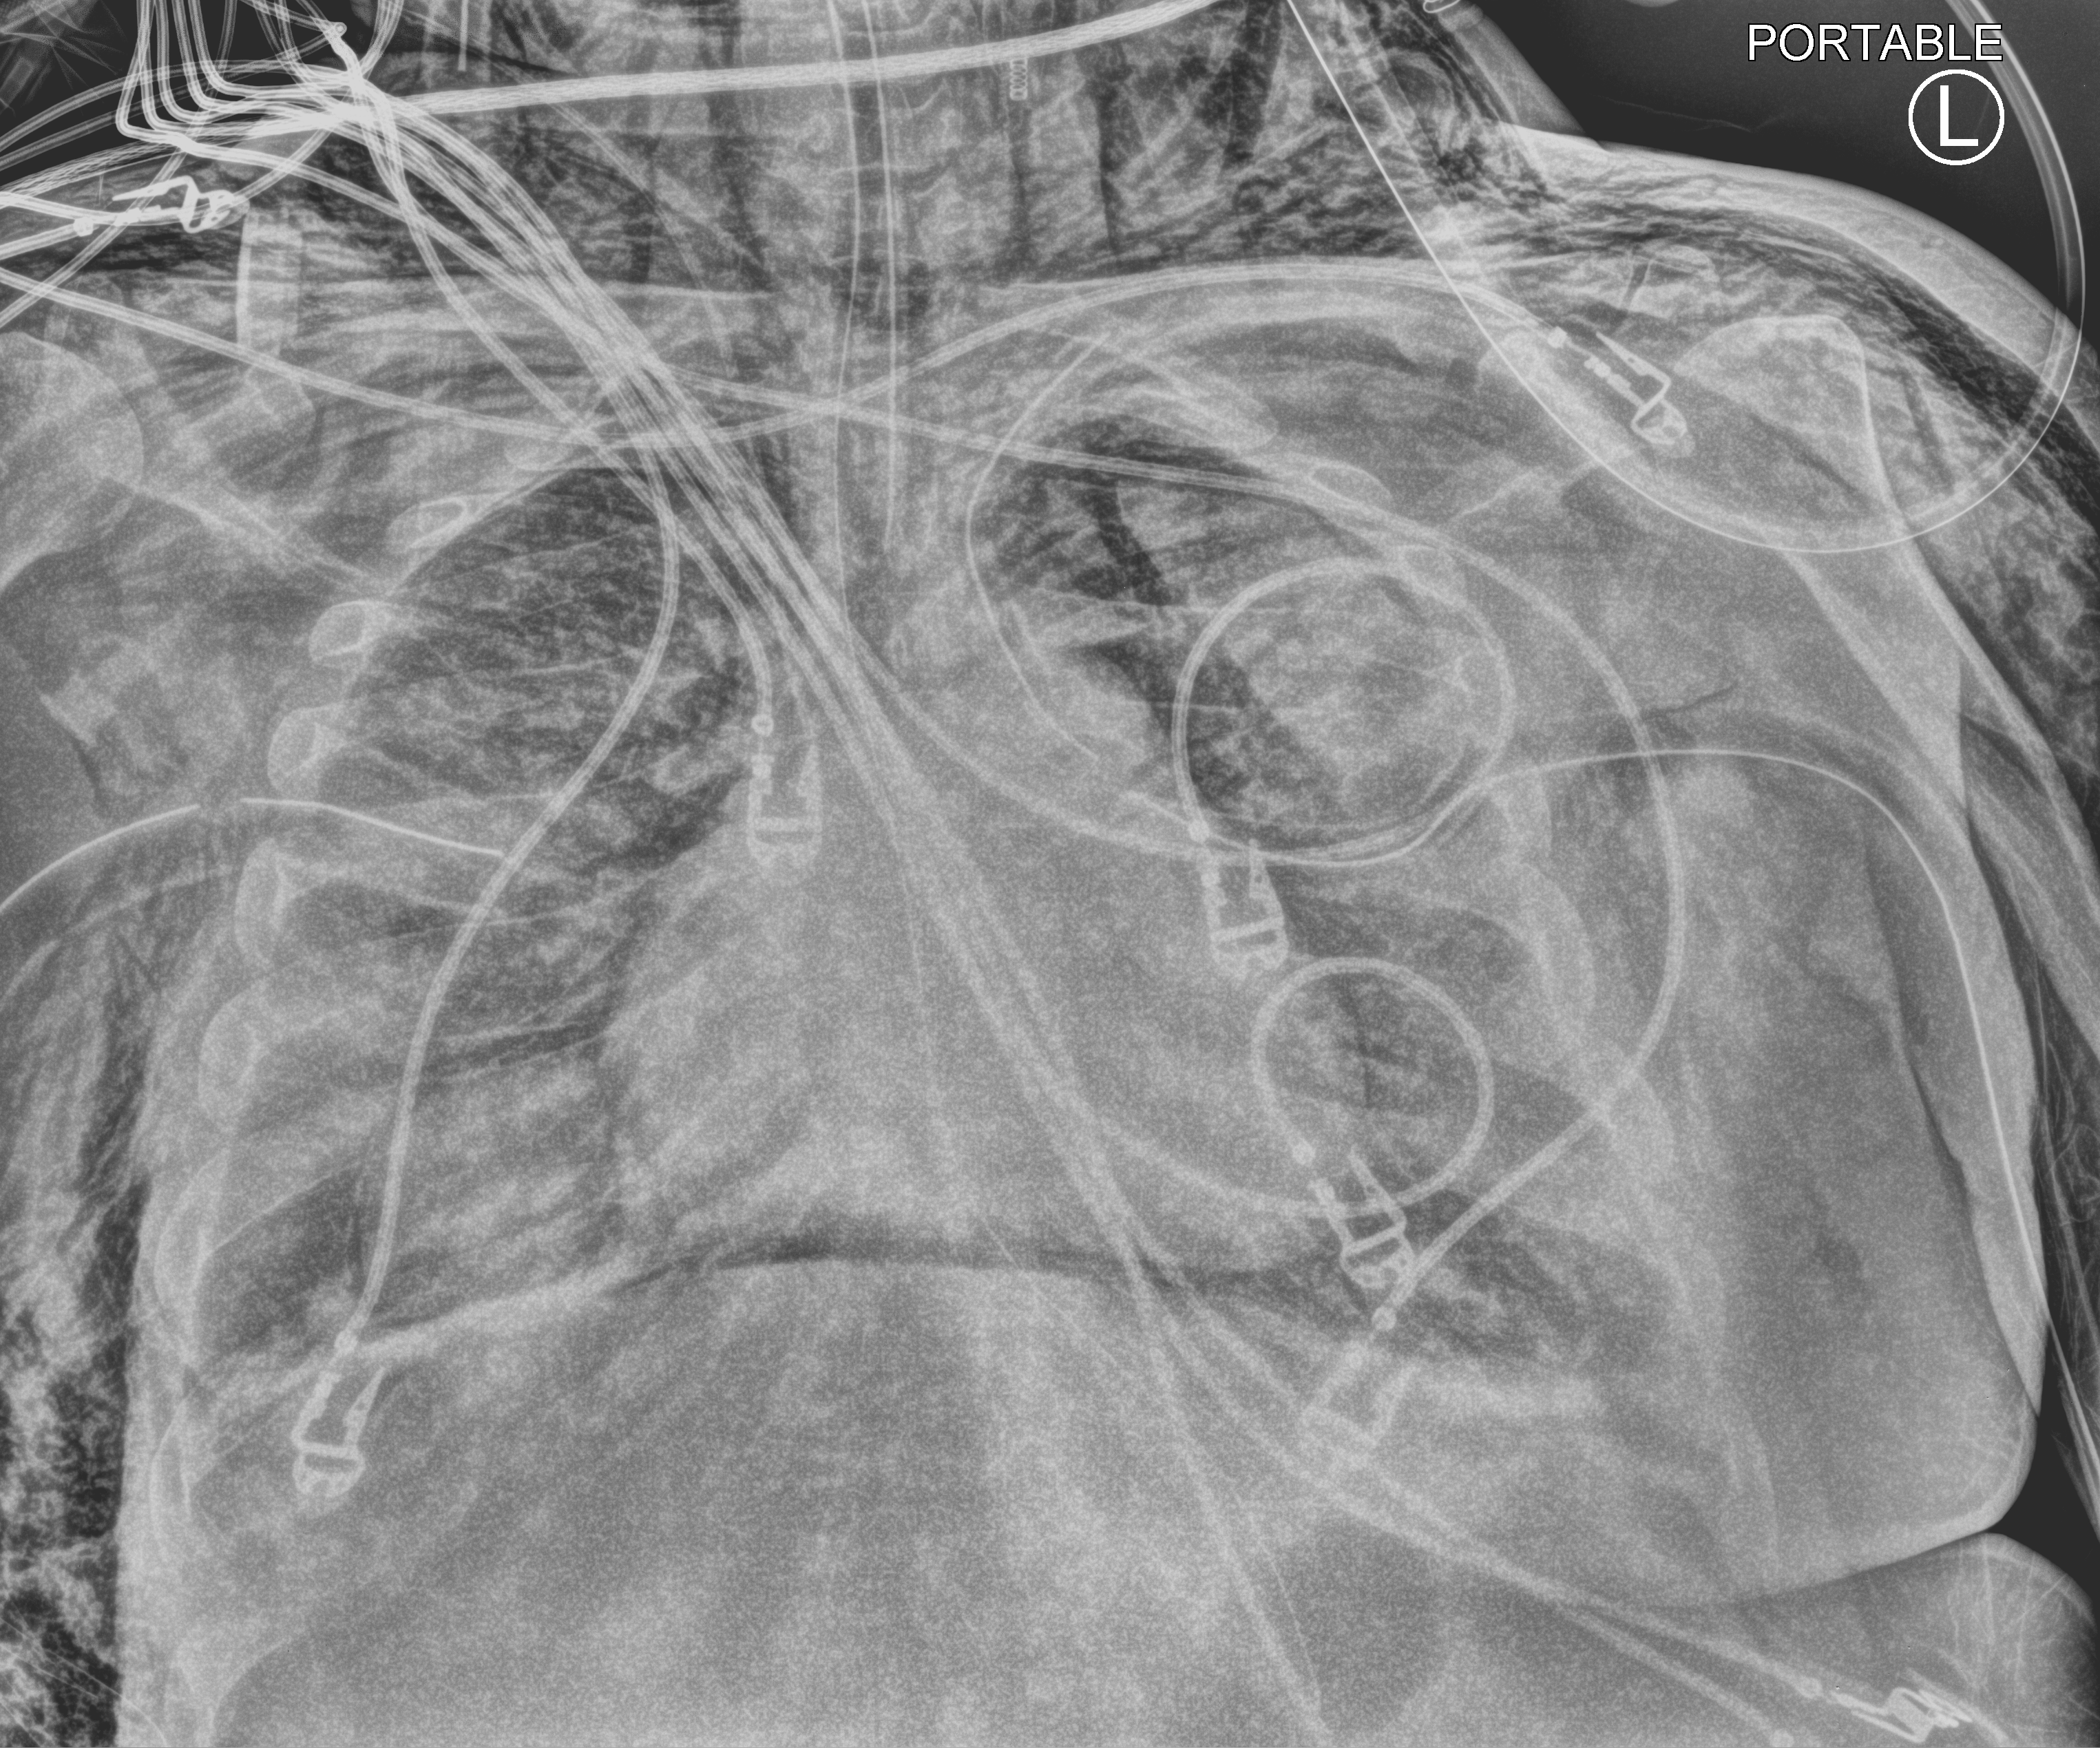
Bedside chest radiograph (computed radiography), anteroposterior (AP) projection. Adult patient hospitalised with COVID-19, age 18–59 years.
Admission-level facts for this patient (not findings on this image; timing relative to this image not recorded):
- admitted to intensive care during this hospital stay: yes